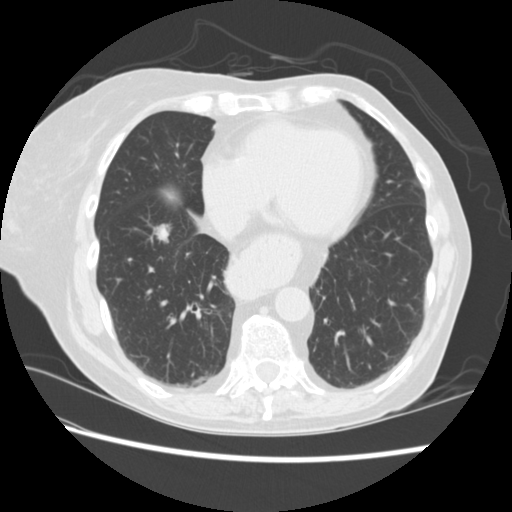
Low-dose screening chest CT, one axial slice. Slice 69 of 224 in the series (ordered by position). Reconstruction kernel STANDARD. 120 kVp. Lung window (W 1500 / L -600 HU). 512 × 512 image matrix, field of view 340 × 340 mm.
Outlined on this slice (manually delineated by an expert):
- lesion 2 (tumor, lower lobe of right lung): bounding box <155,225,169,242> (left, top, right, bottom; pixels)